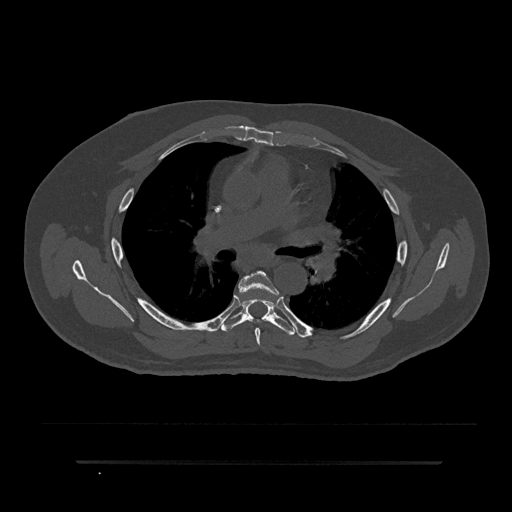
CT including the spine, one axial slice; slice 548 of 797 in the series (ordered by position); reconstruction kernel Br40s/3; bone window (W 1800 / L 400 HU); 512 × 512 image matrix. Patient: male, 59 years. Case-level facts recorded for this patient, not image findings: primary cancer: bile ducts.
Annotated regions visible in this slice (semi-automatic segmentation, software-assisted and operator-edited):
- T5 vertebra: bounding box (x1, y1, x2, y2) in pixels: (239, 271, 278, 346)
- T6 vertebra: (221, 299, 294, 336)